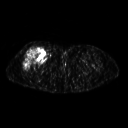
FDG PET of an extremity soft-tissue mass (from a PET/CT study), one axial slice; slice 267 of 311 in the series (ordered by position); 3.27 mm slice thickness; 128 × 128 image matrix, field of view 500 × 500 mm. Patient: female, 57 years. Case-level facts recorded for this patient, not image findings: histological type: pleiomorphic undifferentiated sarcoma; grade: high; site of the primary tumour: right quadricep.
Structures marked on this image (expert contour drawn on MRI and transferred to this co-registered scan by the dataset authors):
- tumour plus oedema (research contour): bounding box [x1, y1, x2, y2] px = [23, 47, 46, 70]
- tumour (research contour): [23, 47, 46, 70]